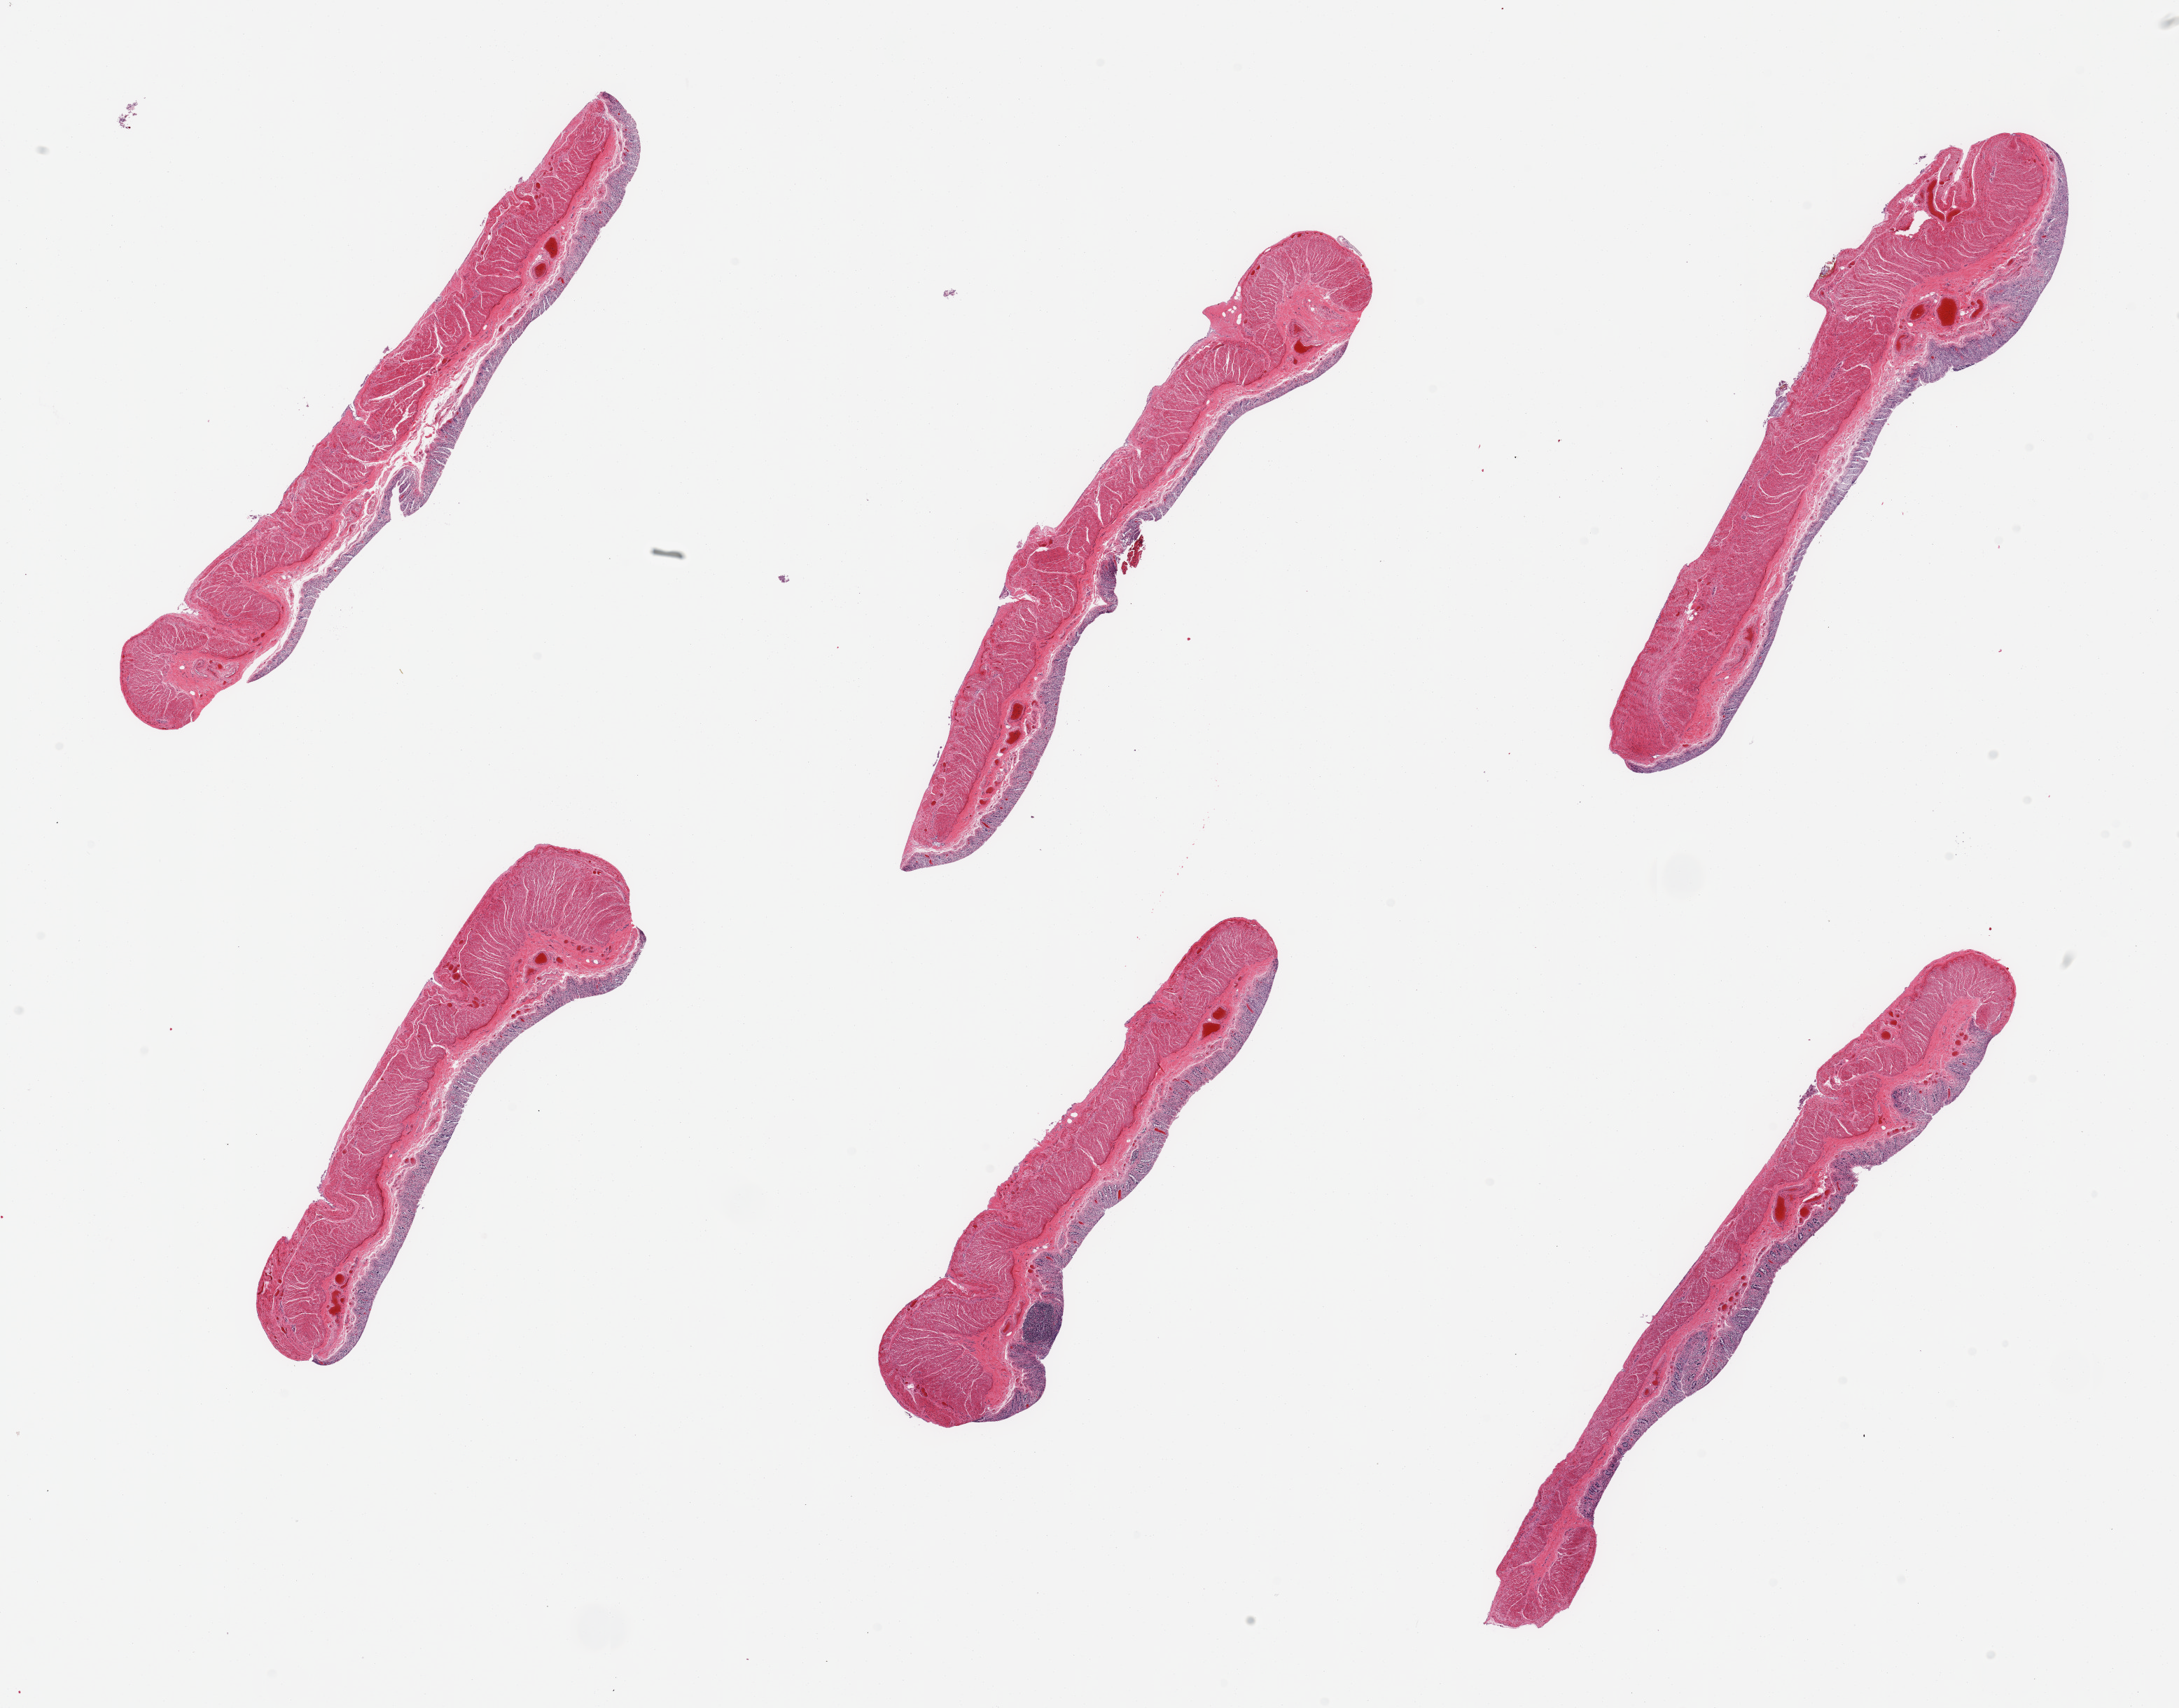
Whole-slide image, haematoxylin and eosin stain, brightfield, low-resolution overview of the scanned area, about 24.6 x 19.3 mm (acquisition: 20x scan). PAXgene-fixed paraffin-embedded (PFPE) section. Sampled site (target tissue): transverse colon. Tissue donor sample. Donor: male.
* pathologist's review note for this sample: 6 pieces, mucosa up to ~0.15mm, glandular mucosa totally autolyzed